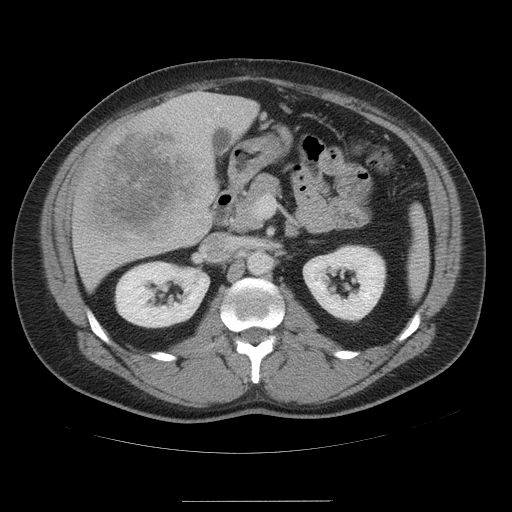
Contrast-enhanced abdominal CT, one axial slice; slice 25 of 54 in the series (ordered by position); 120 kVp; intravenous contrast given; soft-tissue window (W 400 / L 40 HU); 512 × 512 image matrix, field of view 436 × 436 mm. Male patient, age 40 years. Case-level facts recorded for this patient, not image findings: diagnosis: colorectal cancer liver metastases, imaged before liver resection; multiple liver metastases: no; largest metastasis: 15 cm; disease in both lobes: no.
Outlined on this slice (outlined manually by an expert reader):
- liver: bounding box [x1, y1, x2, y2] px = [73, 92, 258, 289]
- planned liver remnant (the part of the liver to remain after resection): [222, 96, 258, 134]
- liver metastasis: [84, 126, 206, 249]